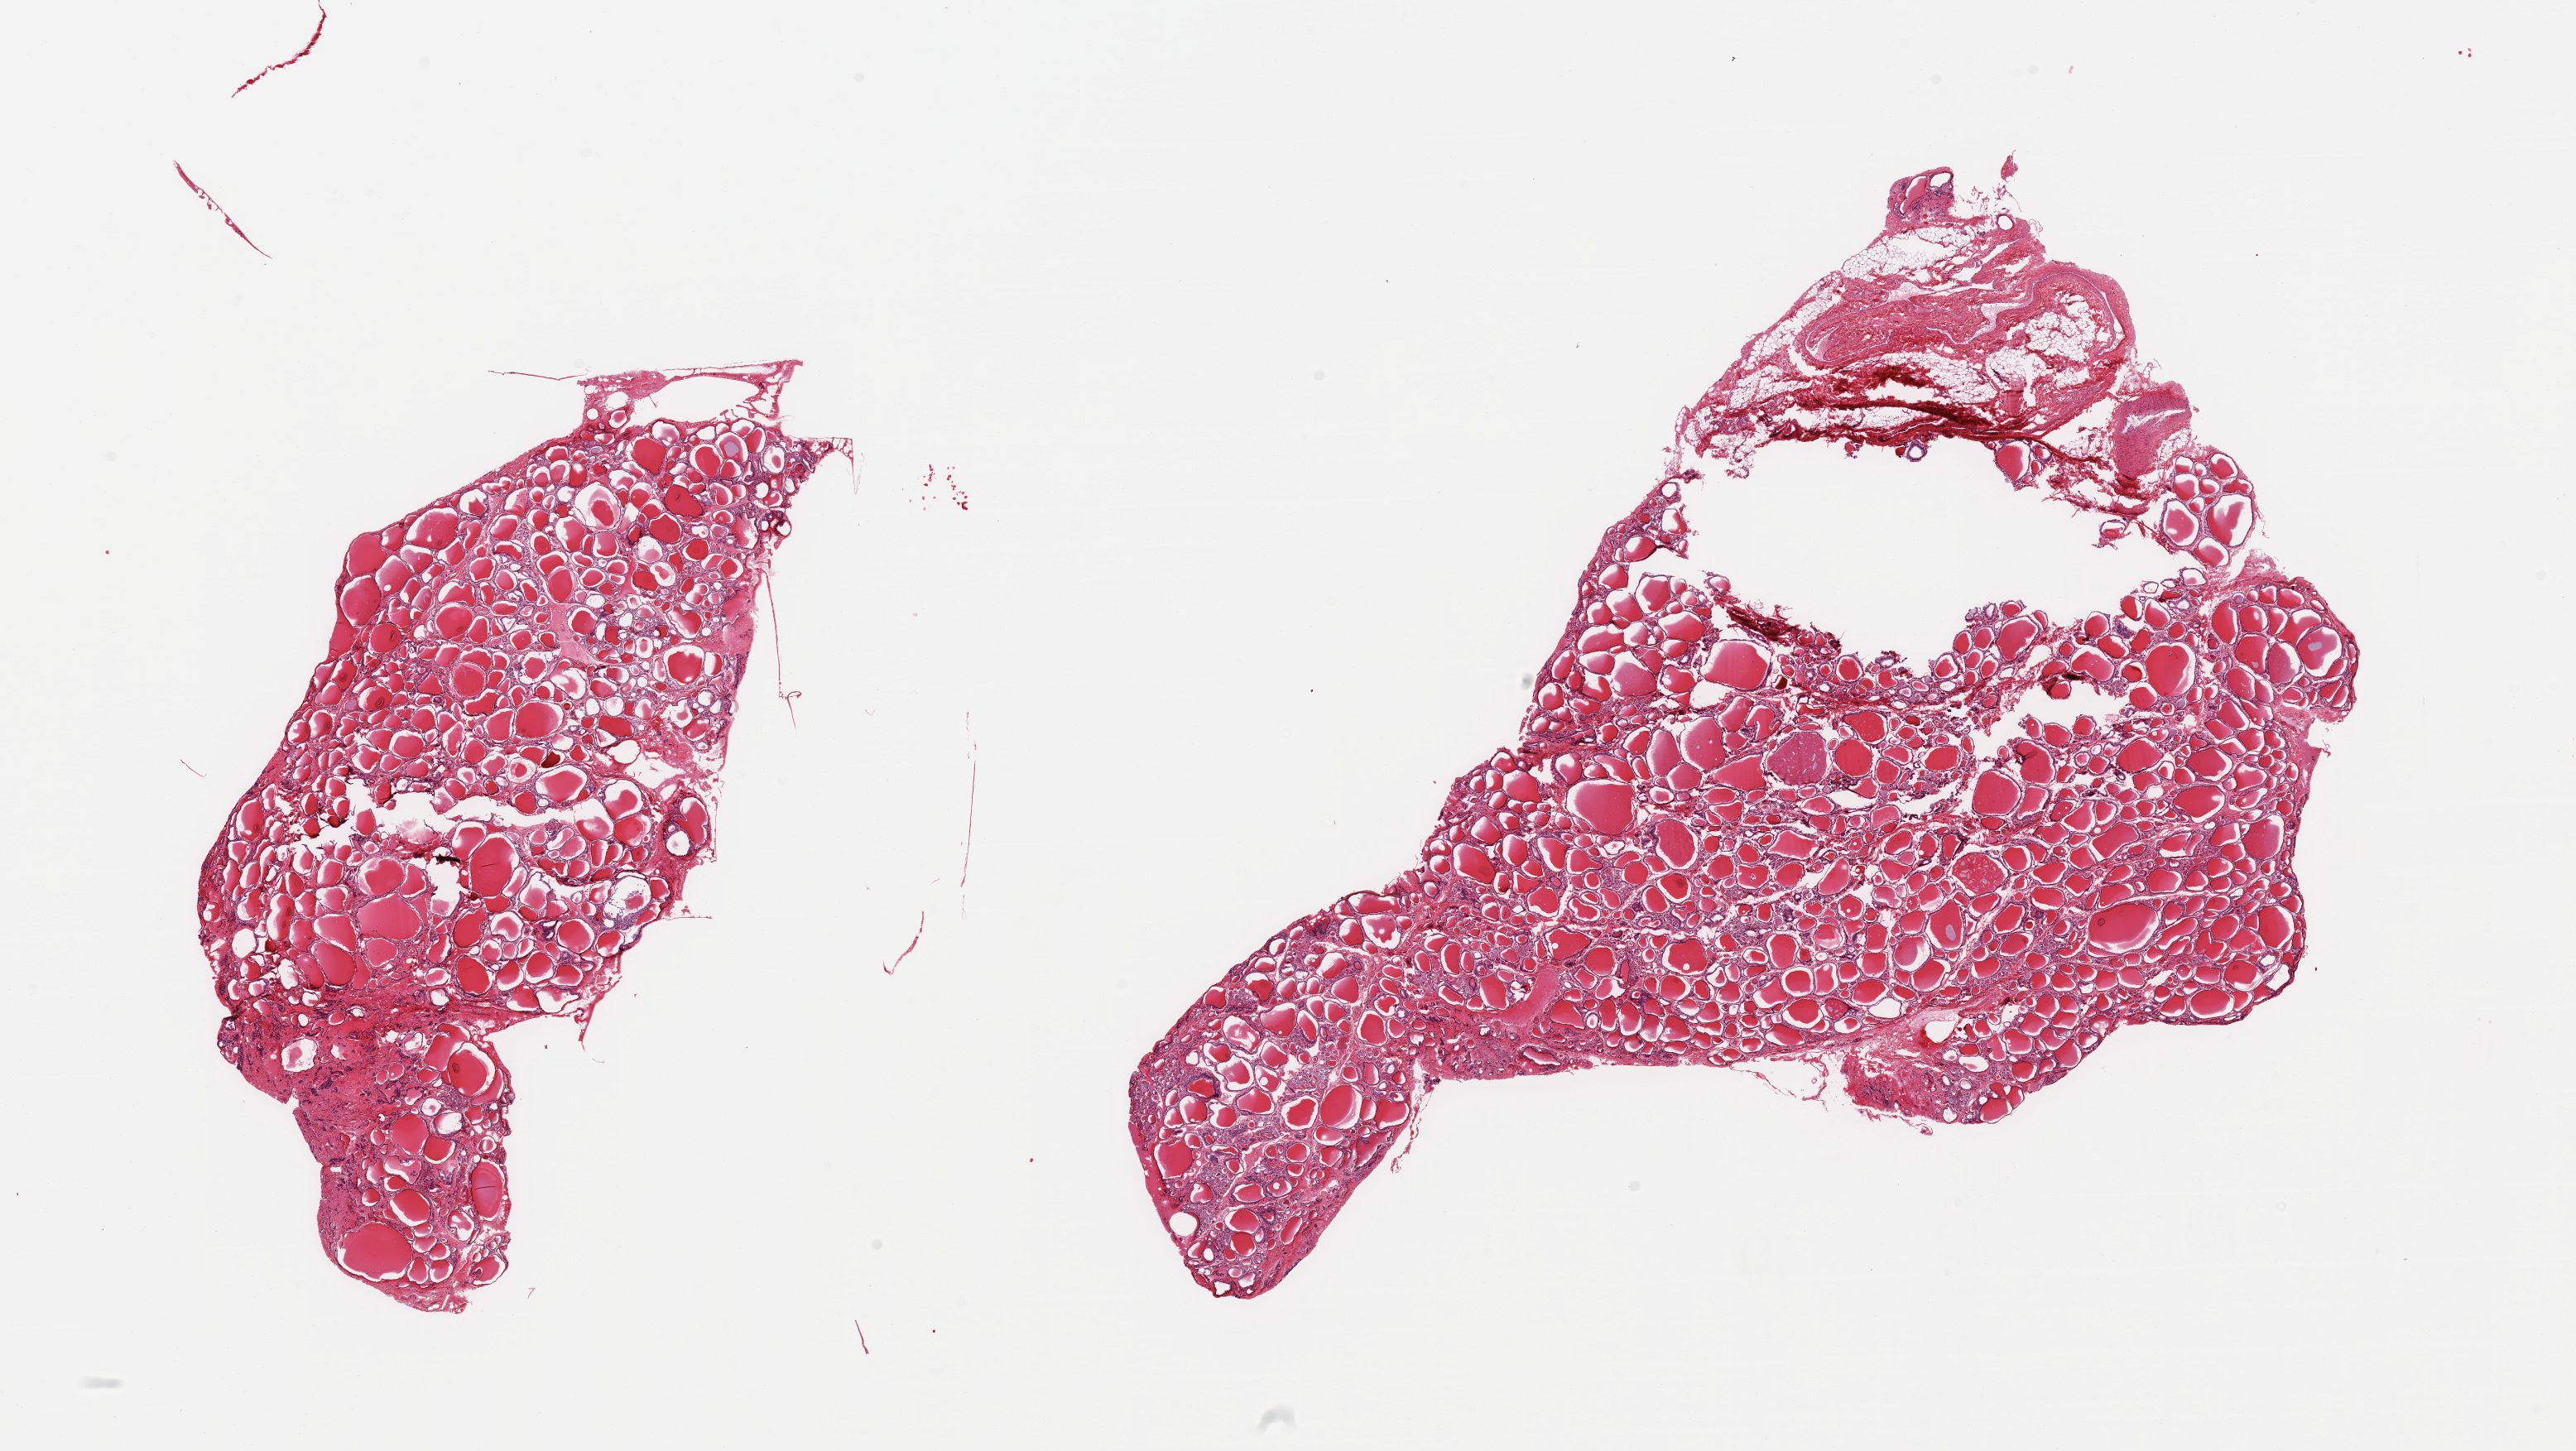
Whole-slide image, haematoxylin and eosin stain, brightfield, shown as a low-resolution overview of the whole scanned area (about 24.6 x 13.9 mm); PAXgene-fixed, paraffin-embedded tissue; sampled site (target tissue): thyroid; tissue donor sample. Male donor.
* pathologist's review note for this sample: 2 pieces; one piece includes ~10% fat/vessels, some regressive changes